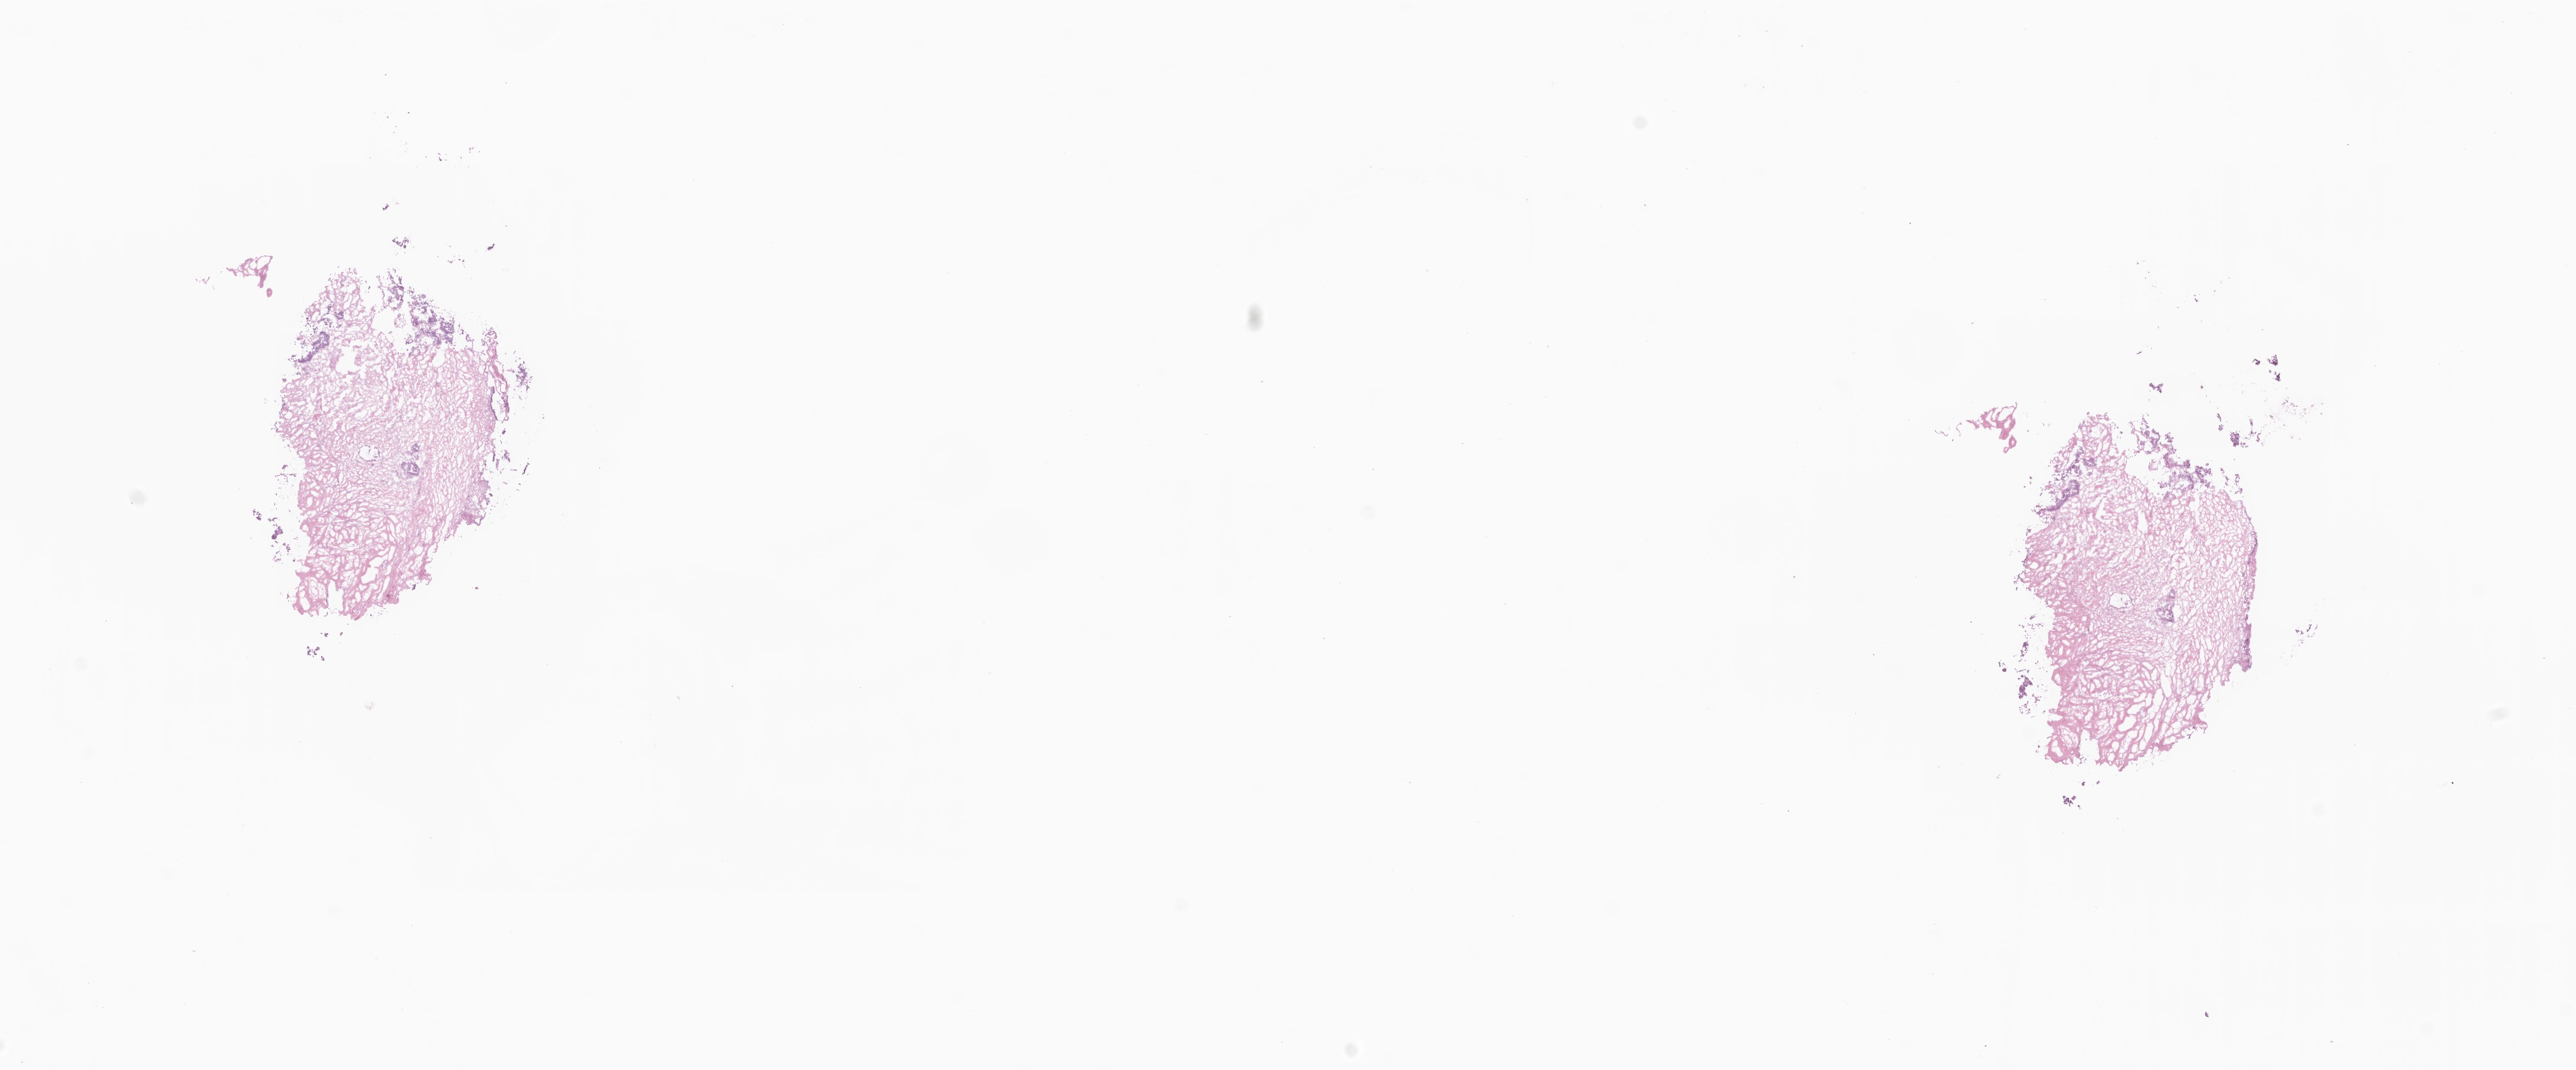
Whole-slide image, H&E stain, shown as a low-resolution overview of the whole scanned area (about 18.1 x 7.5 mm); frozen section (tissue freezing medium); metastatic tumor tissue, resected from pelvis. Male patient; age at initial diagnosis 61 years. Pathologist review of this section (percent, as recorded): tumor cells 5%, tumor nuclei 90%, stromal cells 93%, necrosis 2%, normal cells 0%. Inflammatory infiltration, as recorded: lymphocyte infiltration 2%, monocyte infiltration 0%, neutrophil infiltration 0%.
Section: bottom of the tissue portion. Patient diagnosis (primary): Adenocarcinoma, NOS.